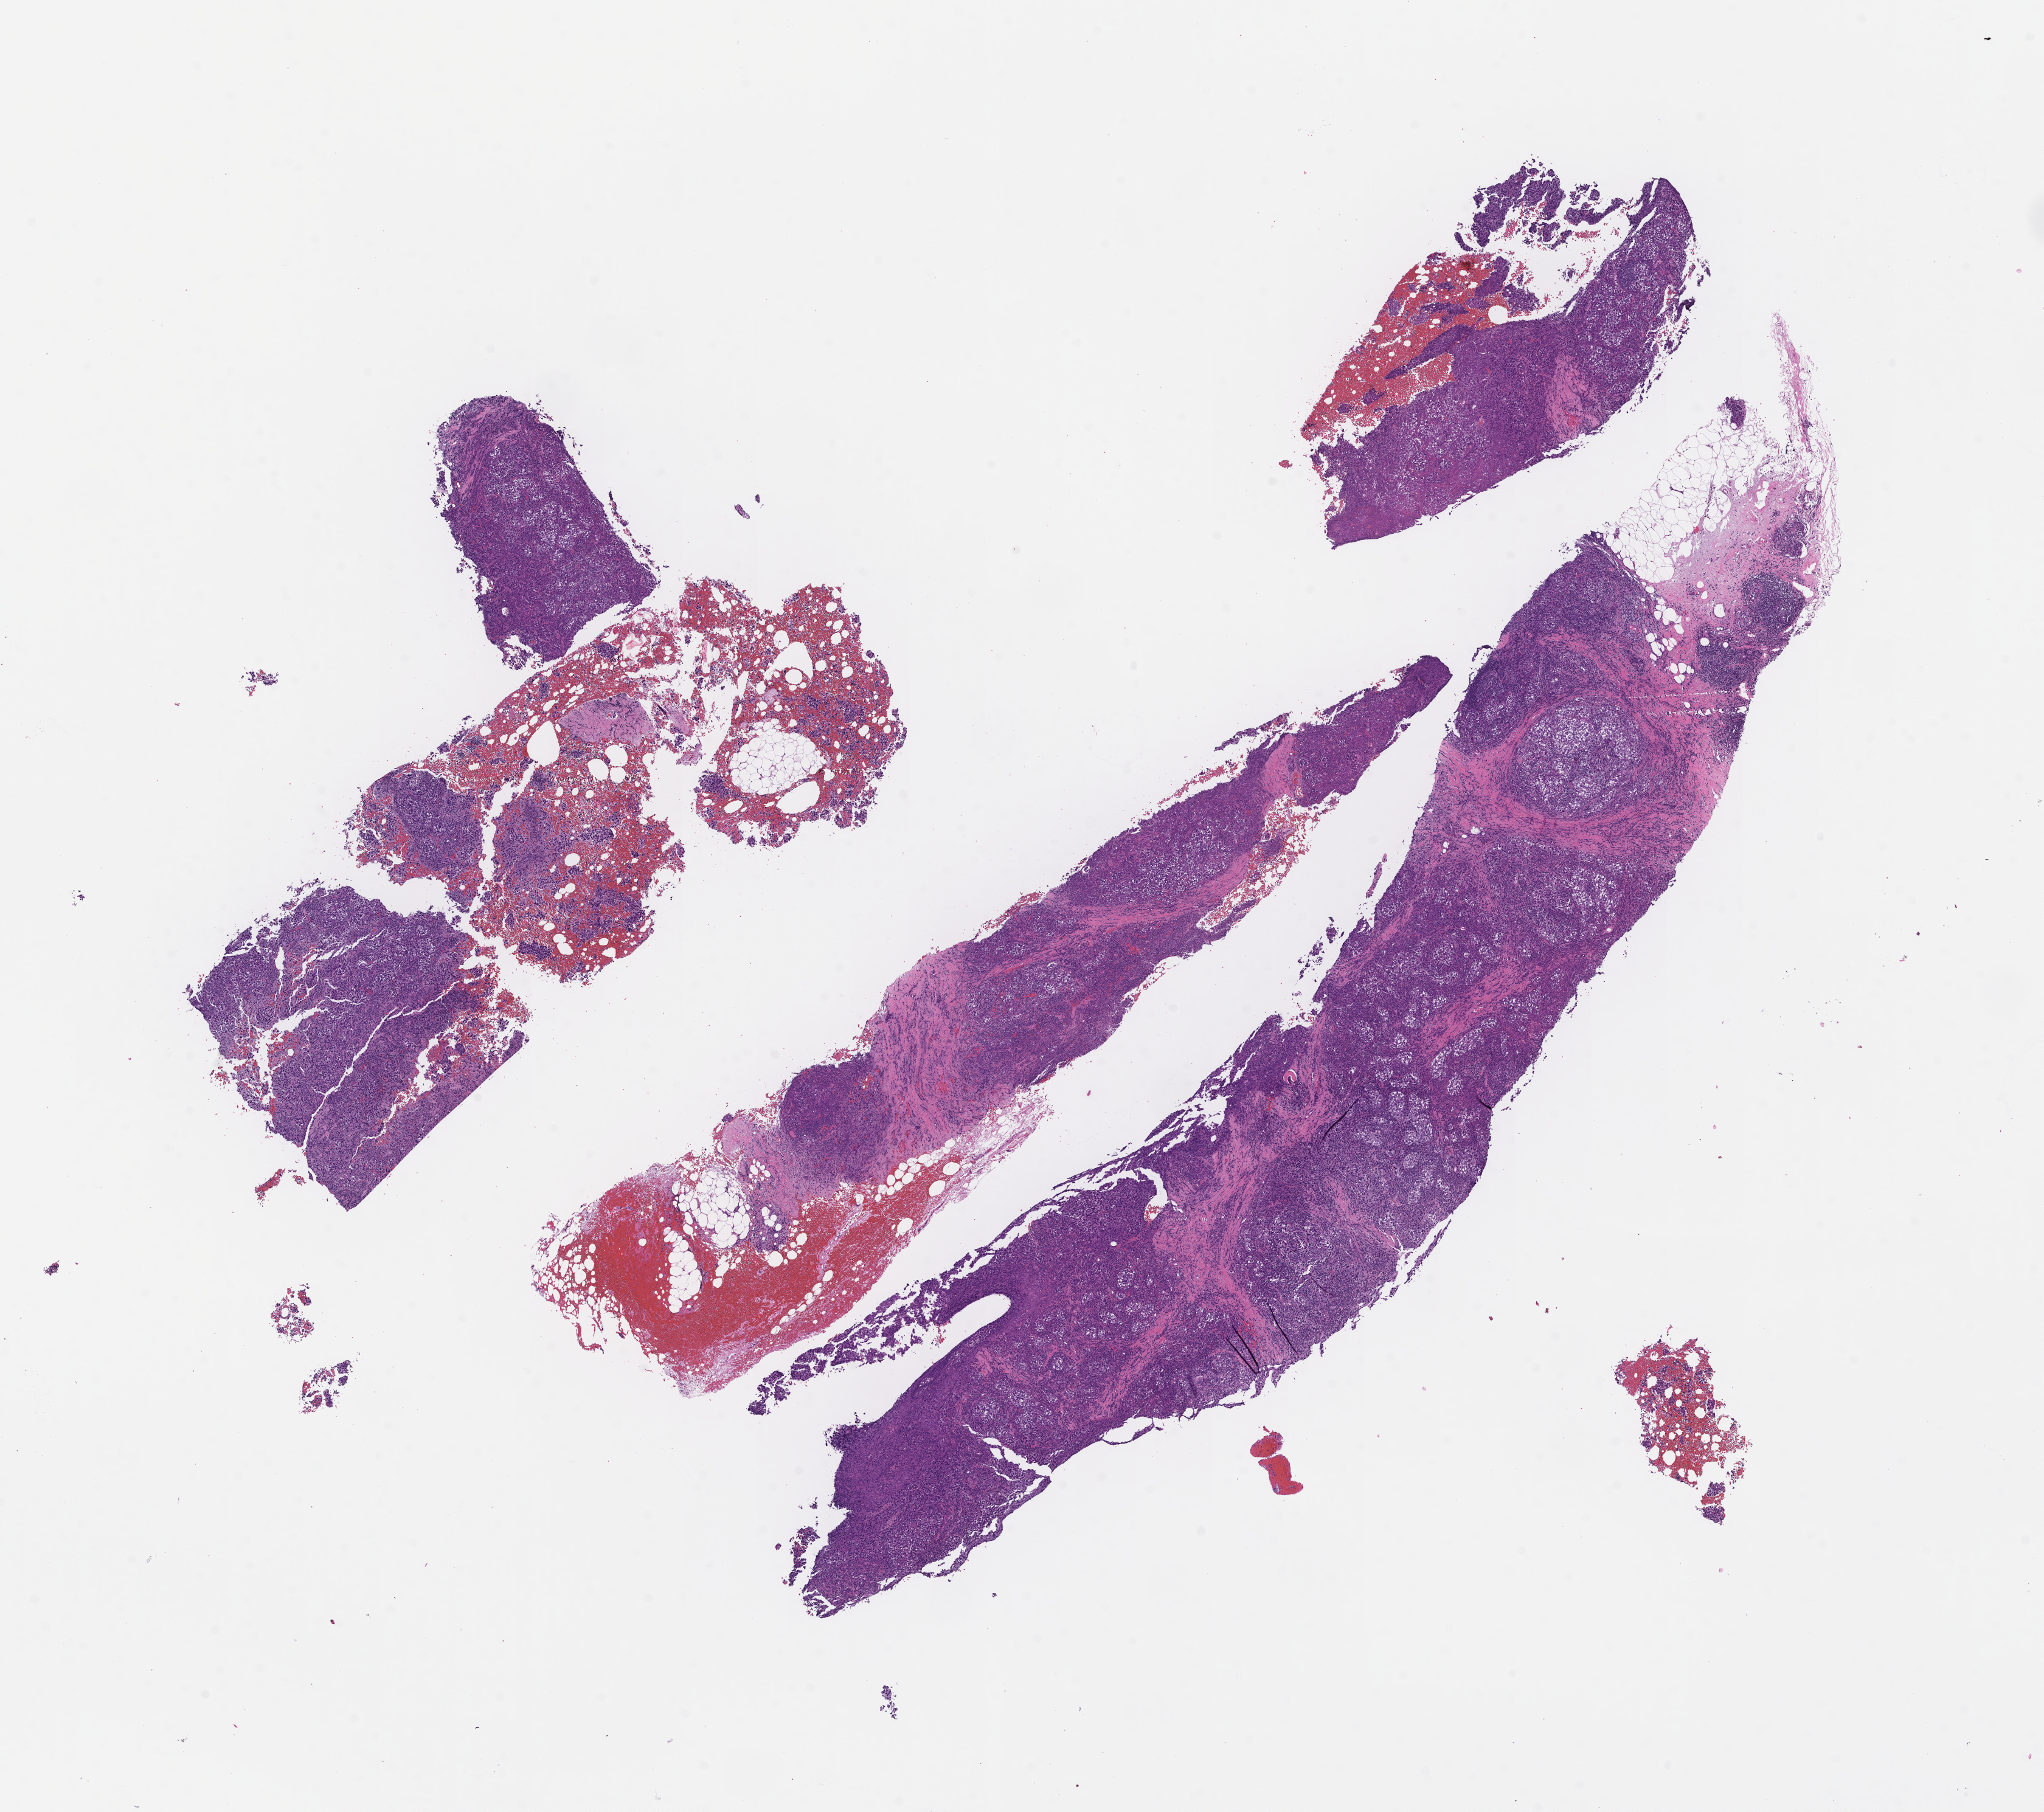
Whole-slide image, haematoxylin and eosin stain, whole scanned area (about 13.6 x 12.0 mm) shown as a low-resolution overview, formalin-fixed, paraffin-embedded (FFPE) tissue, archival tissue. Female patient.
- this section: metastasis (sampled organ not recorded)
- primary diagnosis of the patient: Invasive Breast Carcinoma